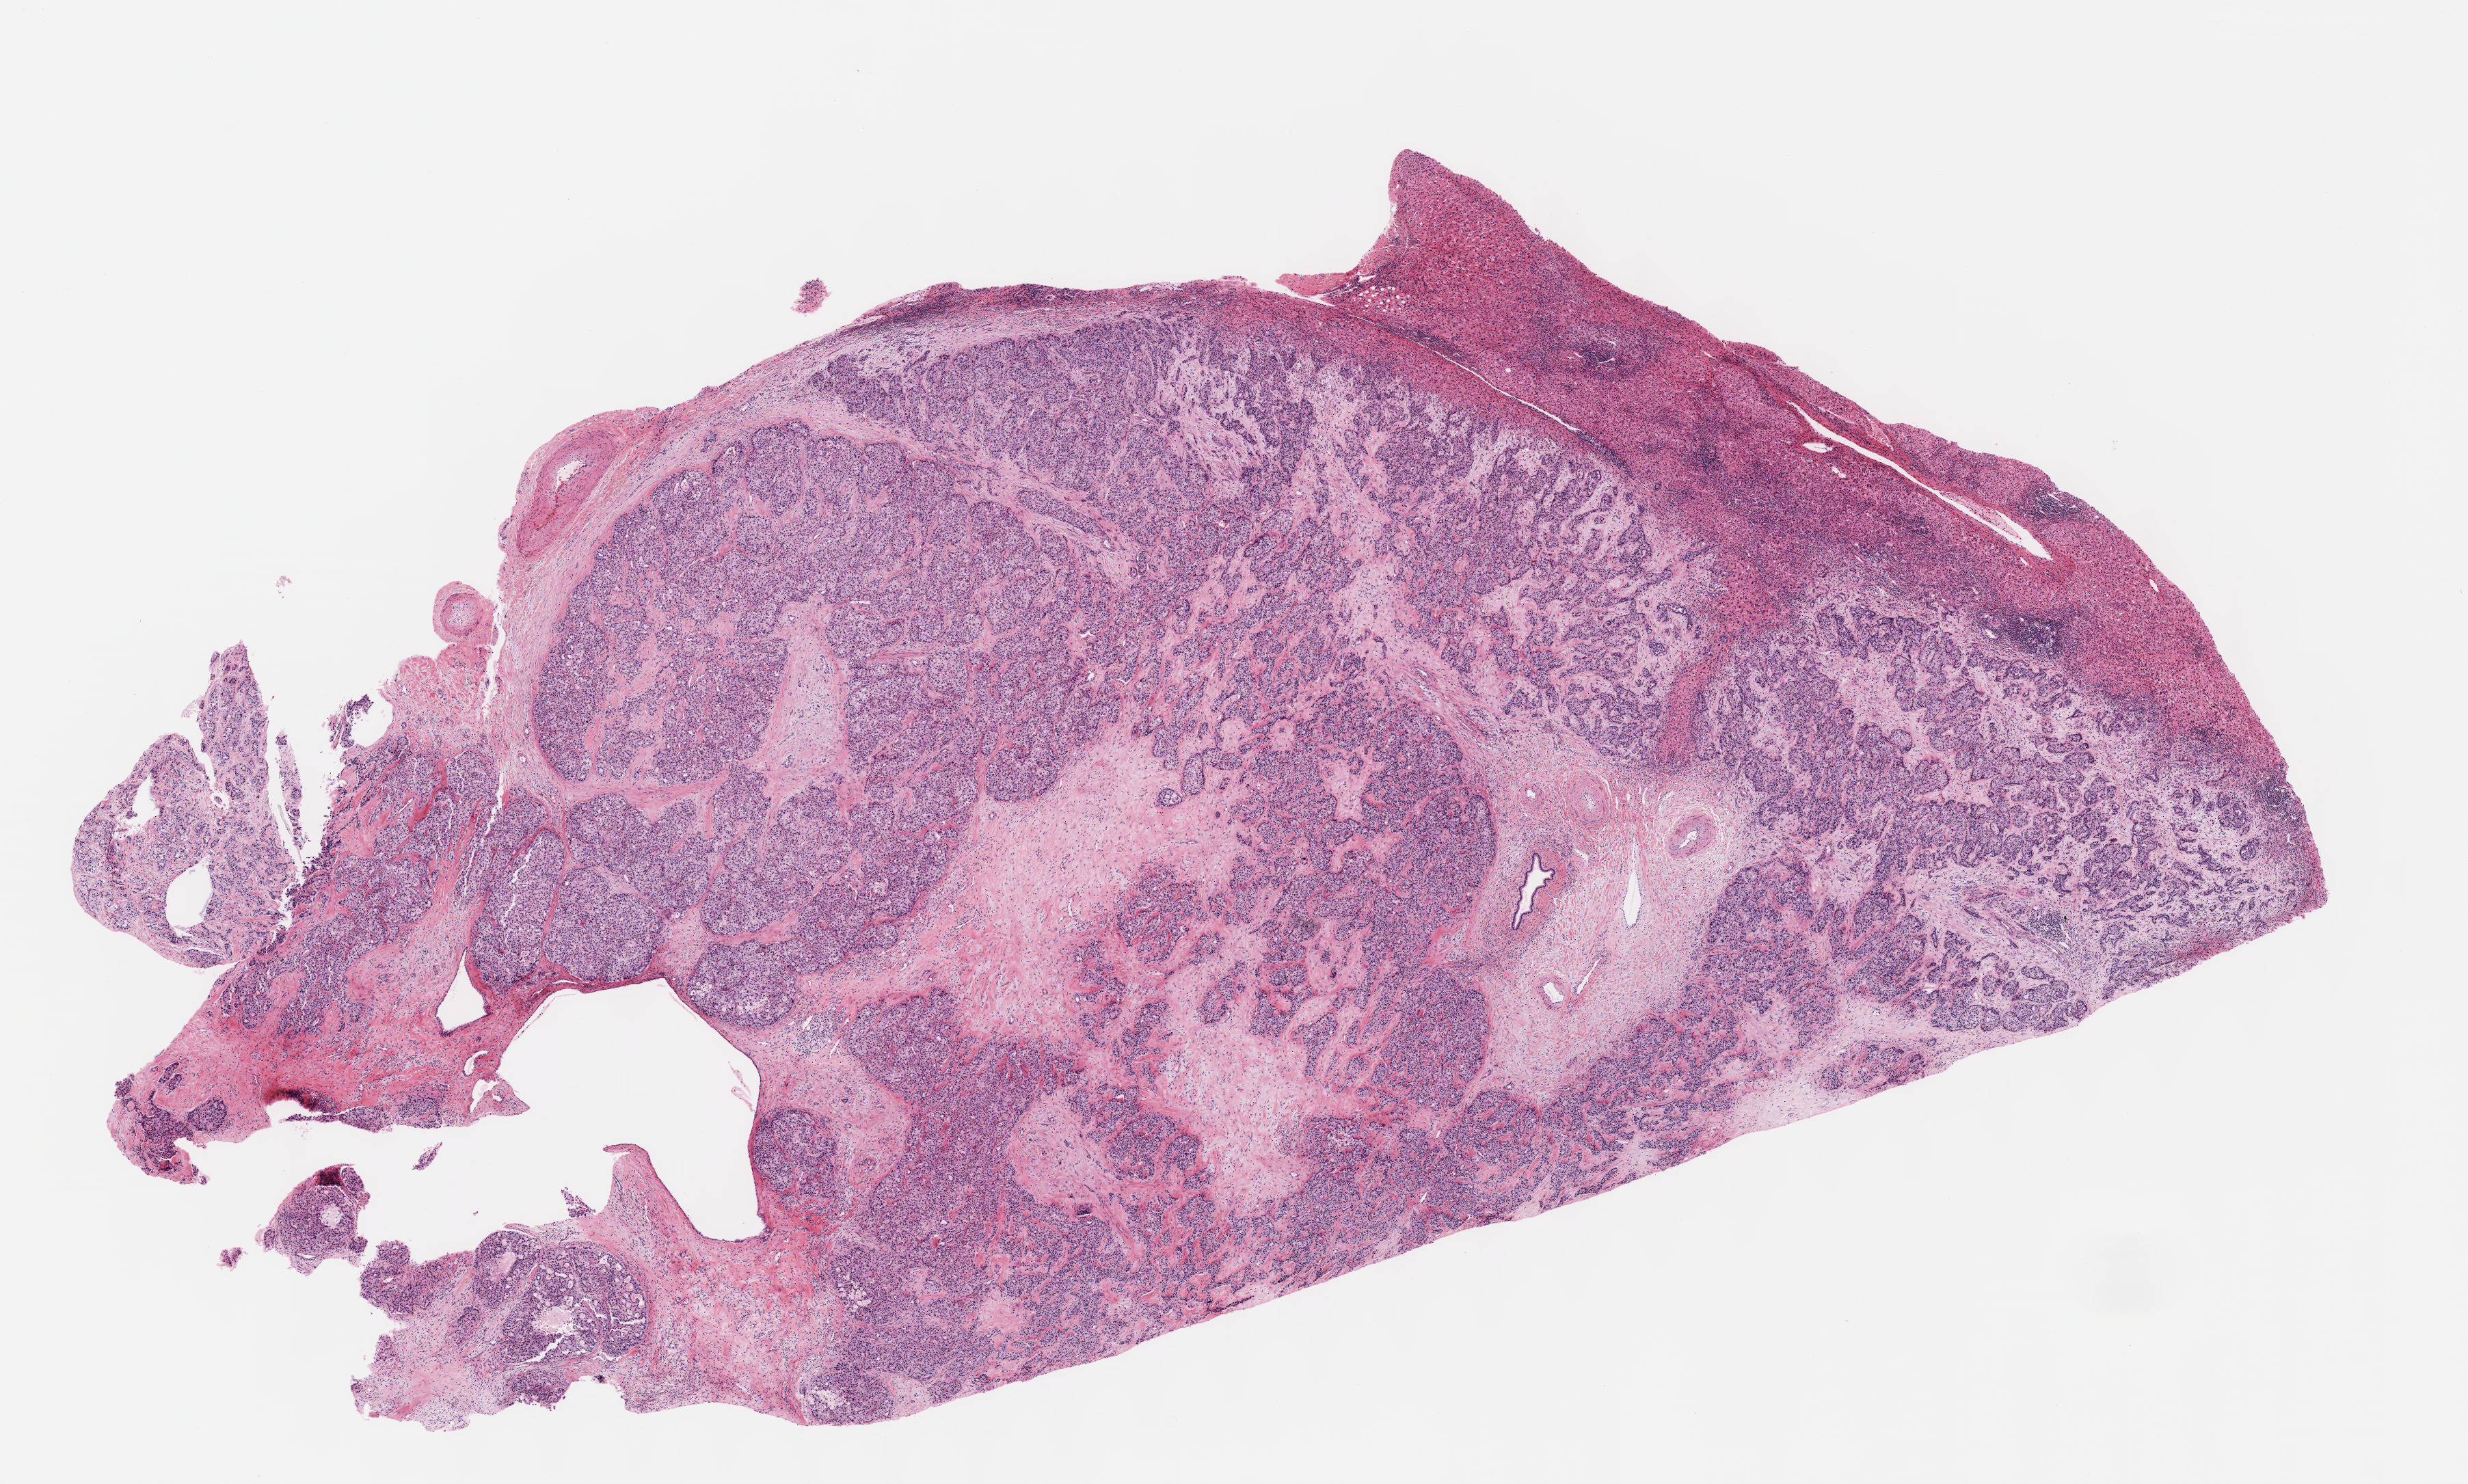
Digitized H&E-stained tissue section (whole slide) — low-resolution overview of the scanned area, about 14.6 x 8.8 mm; FFPE section; liver, primary tumour sample. Female patient; age at initial diagnosis 45 years. Histologic grade: G4 (undifferentiated).
* AJCC pathologic stage: IIIA (7th edition)
* pathologic diagnosis: Hepatocellular carcinoma, NOS